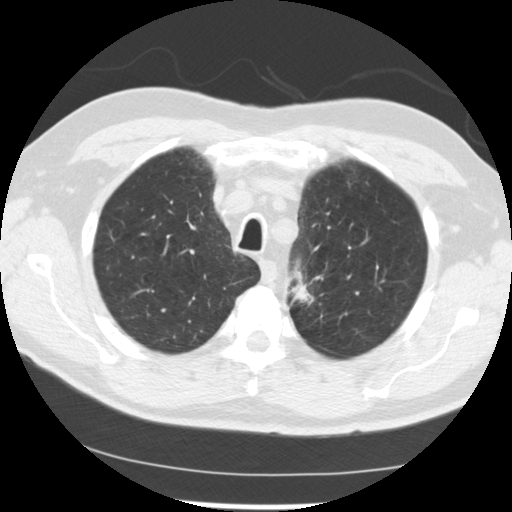
Low-dose screening chest CT, one axial slice; slice 198 of 249 in the series (ordered by position); 120 kVp; lung window (W 1500 / L -600 HU); 2.5 mm slice thickness; 512 × 512 image matrix.
Annotated regions visible in this slice (expert manual segmentation):
- lesion 2 (tumor, upper lobe of left lung): bounding box [x1, y1, x2, y2] px = [294, 282, 314, 303]